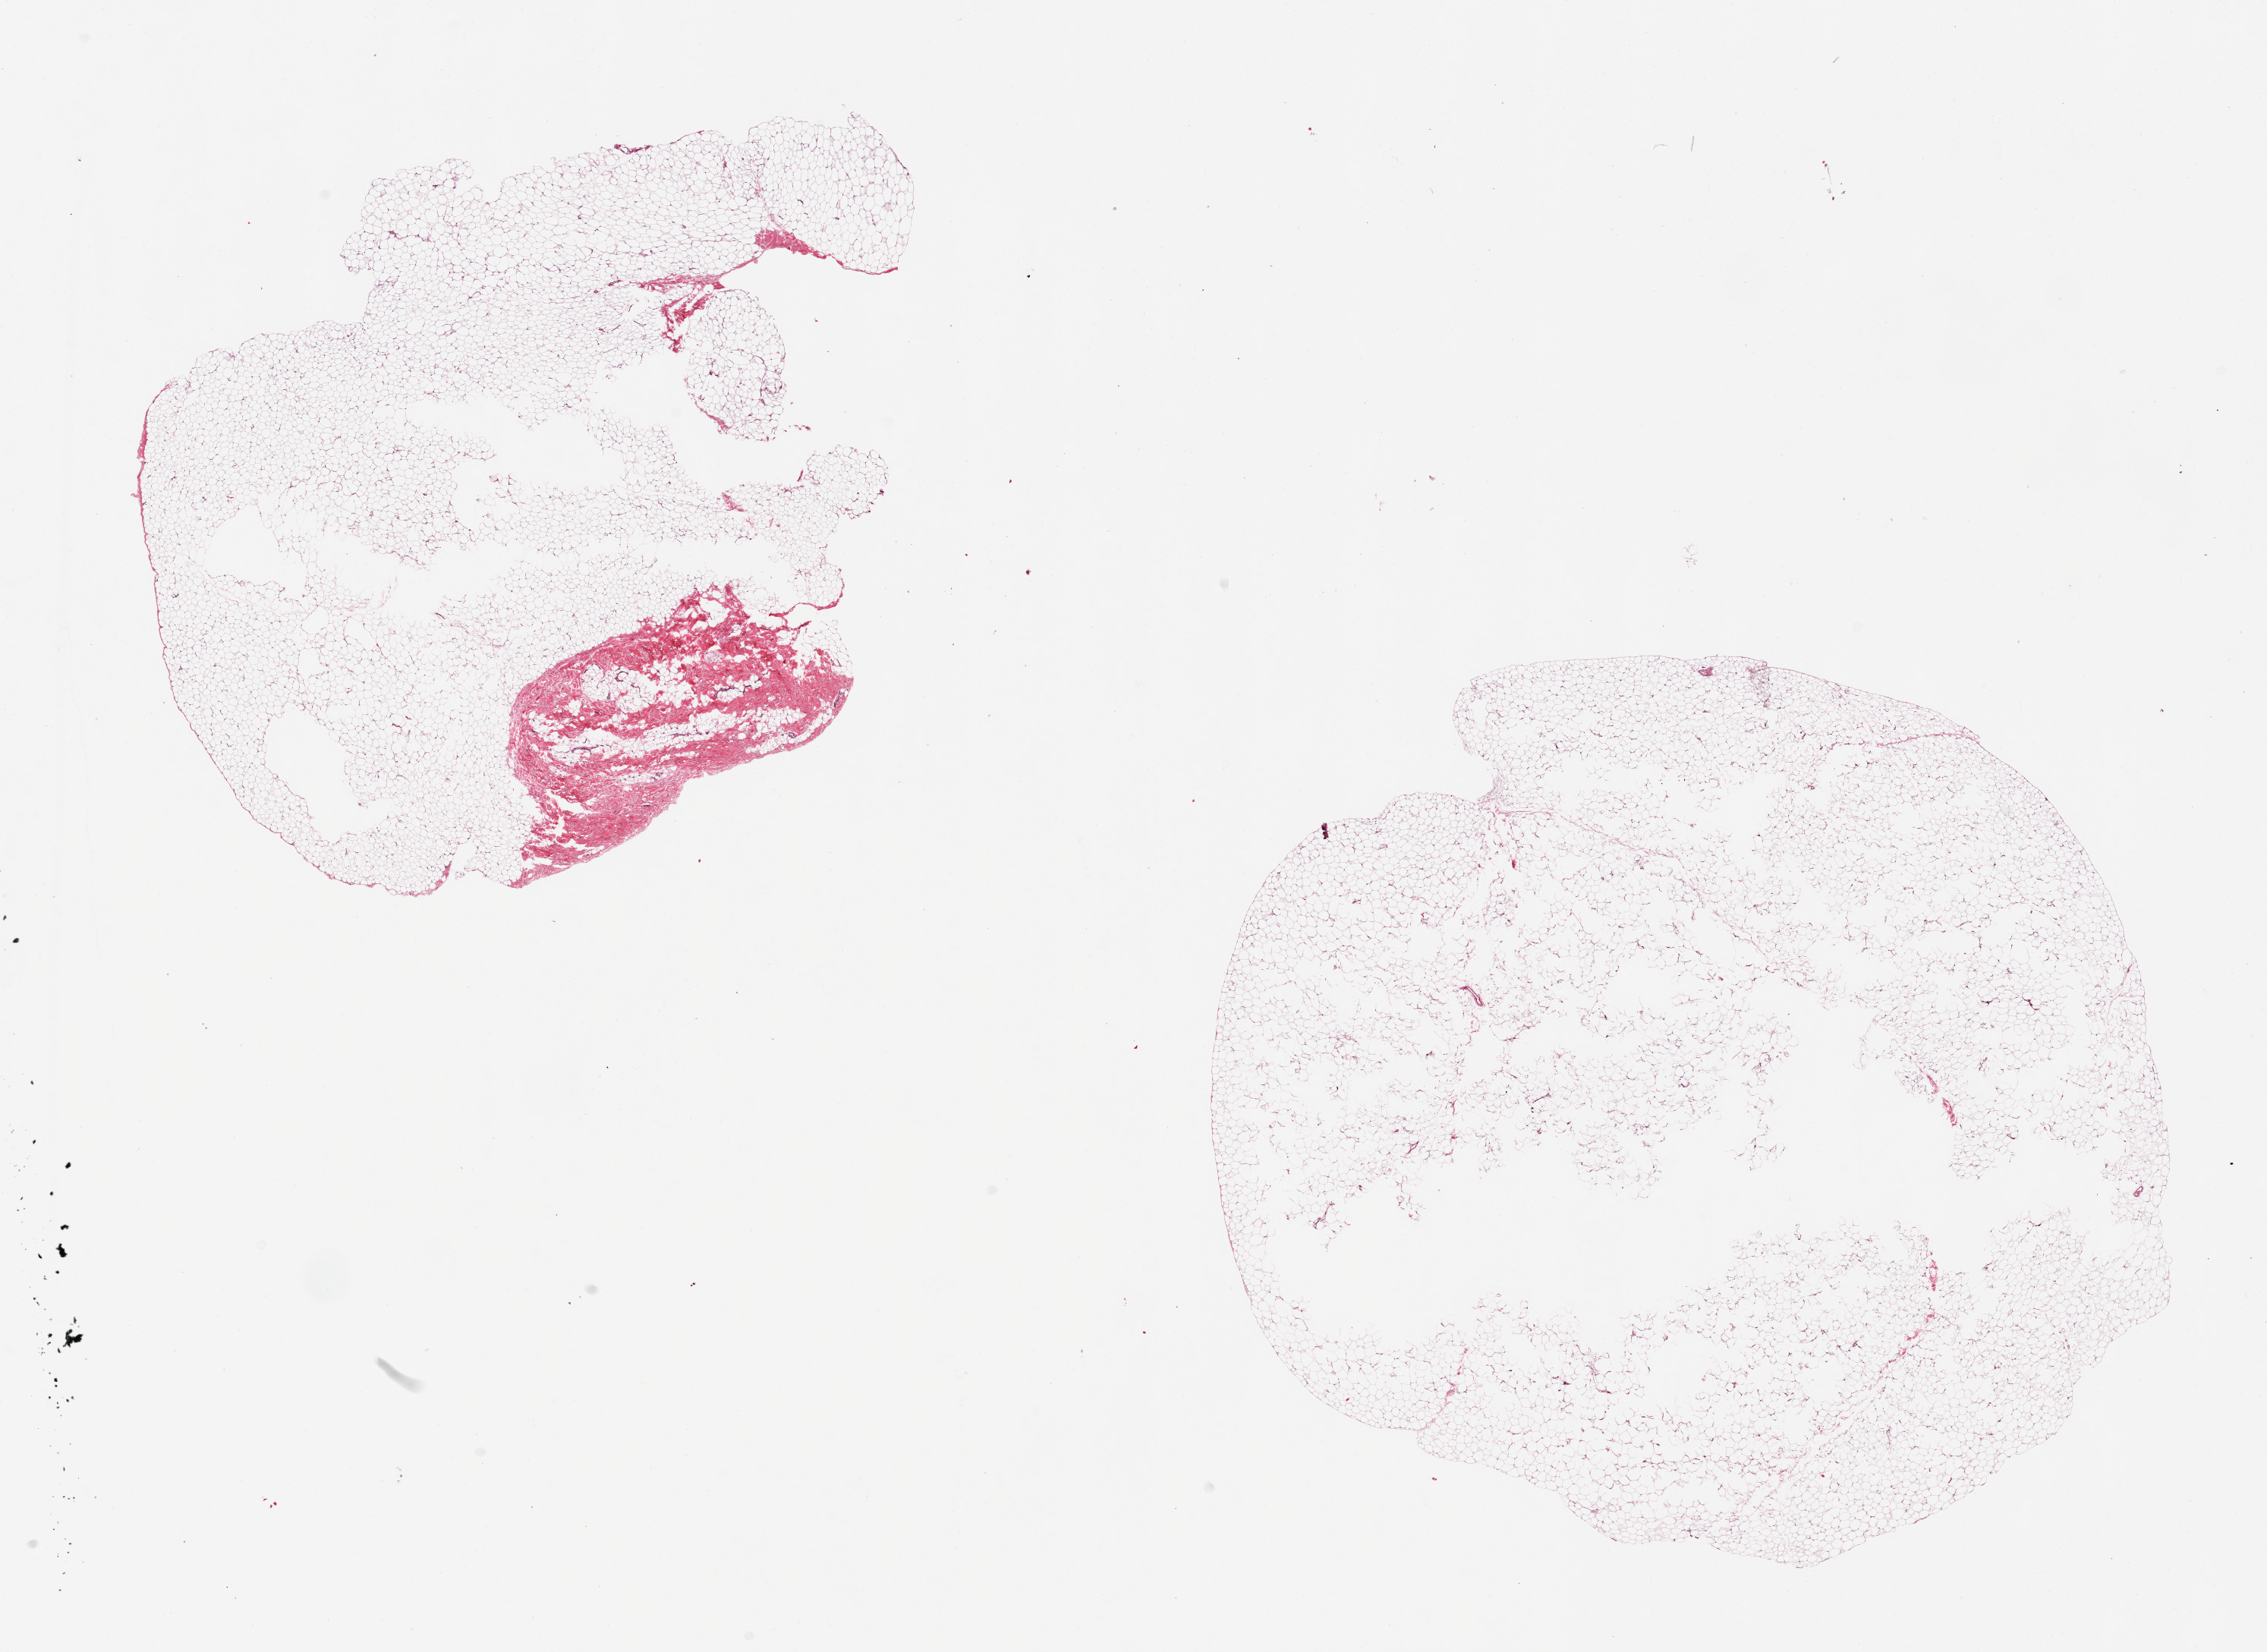
Whole-slide image, haematoxylin and eosin stain, whole scanned area (about 23.6 x 17.2 mm, from a 20x scan) shown as a low-resolution overview. PAXgene-fixed, paraffin-embedded tissue. Section of breast (target tissue). Donor tissue sample.
* reviewer comment on this tissue sample: 2 pieces, one piece ~15% fibrous tissue, defects centrally in both (poor fixation) , essentially no ductal elements